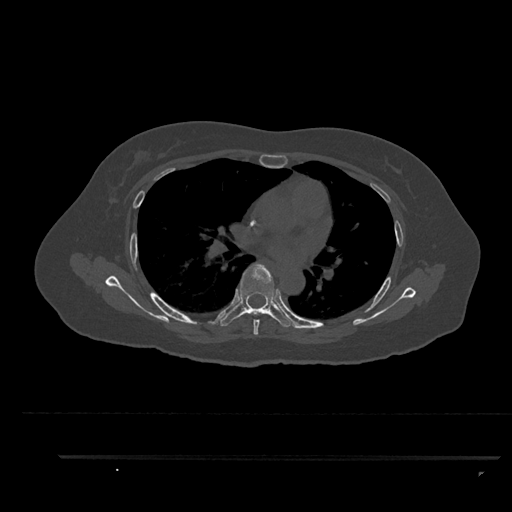
CT including the spine, one axial slice; slice 572 of 797 in the series (ordered by position); reconstruction kernel Br40s/3; 120 kVp; bone window (W 1800 / L 400 HU); 0.5 mm slice thickness; 512 × 512 image matrix, field of view 408 × 408 mm. Female patient, age 44 years. From the clinical record (not read from this slice): primary cancer: renal; vertebrae with lytic lesions (as recorded): L1.
Annotated regions visible in this slice (semi-automatic segmentation, software-assisted and operator-edited):
- T5 vertebra: bounding box [x1, y1, x2, y2] px = [253, 319, 260, 335]
- T6 vertebra: [220, 262, 295, 328]